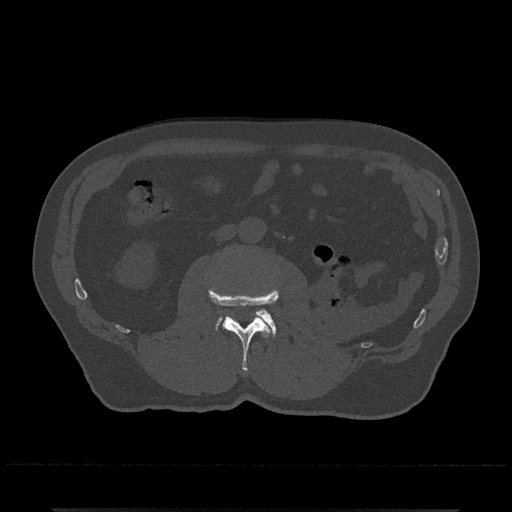
CT including the spine, one axial slice; slice 271 of 797 in the series (ordered by position); bone window (W 1800 / L 400 HU); 0.5 mm slice thickness; 512 × 512 image matrix. Male patient, age 67 years. Case-level facts recorded for this patient, not image findings: primary cancer: prostate.
Outlined on this slice (semi-automatically segmented with operator editing):
- L2 vertebra: bounding box (x1, y1, x2, y2) in pixels: (208, 288, 279, 371)
- L3 vertebra: (217, 309, 276, 337)